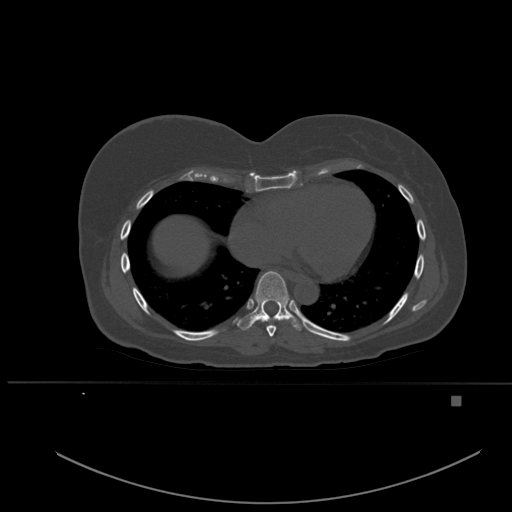
CT including the spine, one axial slice. Position 325 of 651 along the scan axis. Bone window (W 1800 / L 400 HU). 512 × 512 image matrix, field of view 443 × 443 mm. Patient: female, 49 years. From the clinical record (not read from this slice): primary cancer: breast.
Annotated regions visible in this slice (semi-automatically segmented with operator editing):
- T7 vertebra: bounding box (x1, y1, x2, y2) in pixels: (266, 320, 281, 337)
- T8 vertebra: (237, 271, 301, 331)